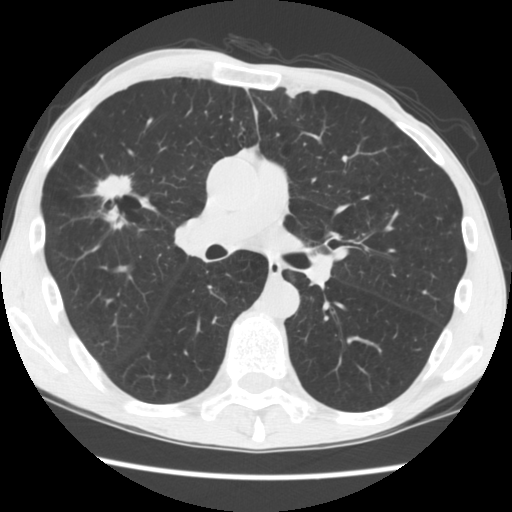
Low-dose screening chest CT, one axial slice; position 99 of 181 along the scan axis; reconstruction kernel STANDARD; lung window (W 1500 / L -600 HU); 2.5 mm slice thickness; 512 × 512 image matrix, field of view 330 × 330 mm.
Annotated regions visible in this slice (outlined manually by an expert reader):
- lesion 1 (tumor, upper lobe of right lung): bounding box <93,175,132,230> (left, top, right, bottom; pixels)